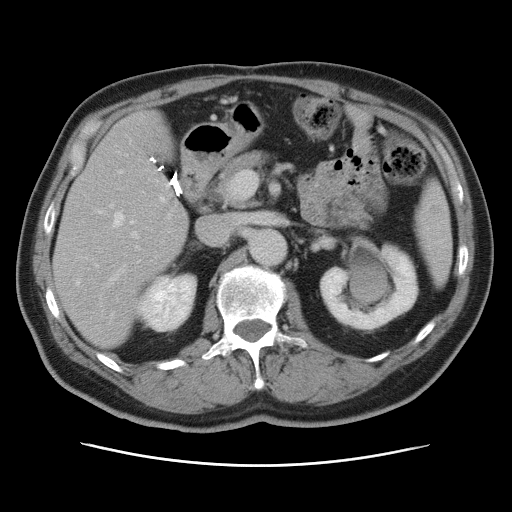
Contrast-enhanced abdominal CT, one axial slice. Position 40 of 80 along the scan axis. 120 kVp. Intravenous contrast given. Soft-tissue window (W 400 / L 40 HU). 5 mm slice thickness. 512 × 512 image matrix. Male patient, age 69 years. From the clinical record (not read from this slice): diagnosis: colorectal cancer liver metastases, imaged before liver resection; multiple liver metastases: no; largest metastasis: 5 cm; disease in both lobes: yes.
Outlined on this slice (expert manual segmentation):
- hepatic veins: bounding box <76,210,134,315> (left, top, right, bottom; pixels)
- liver: <55,112,187,346>
- planned liver remnant (the part of the liver to remain after resection): <55,190,187,346>
- portal vein (with intrahepatic branches): <107,171,141,286>